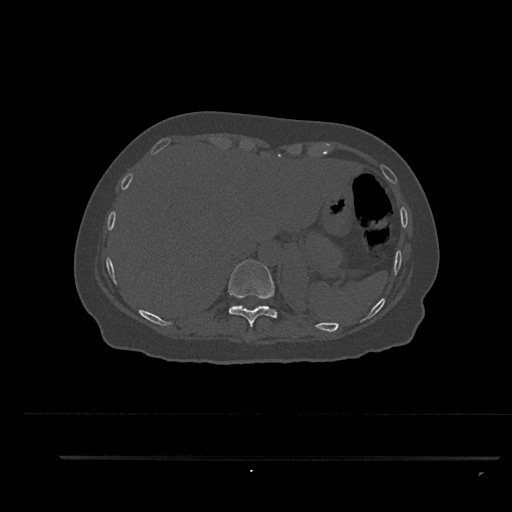
CT including the spine, one axial slice; position 360 of 797 along the scan axis; reconstruction kernel Br40s/3; 120 kVp; bone window (W 1800 / L 400 HU); 0.5 mm slice thickness; 512 × 512 image matrix. Patient: female, 44 years. From the clinical record (not read from this slice): primary cancer: renal; vertebrae with lytic lesions (as recorded): L1.
Outlined on this slice (semi-automatically segmented with operator editing):
- T10 vertebra: bounding box [x1, y1, x2, y2] px = [228, 260, 278, 332]